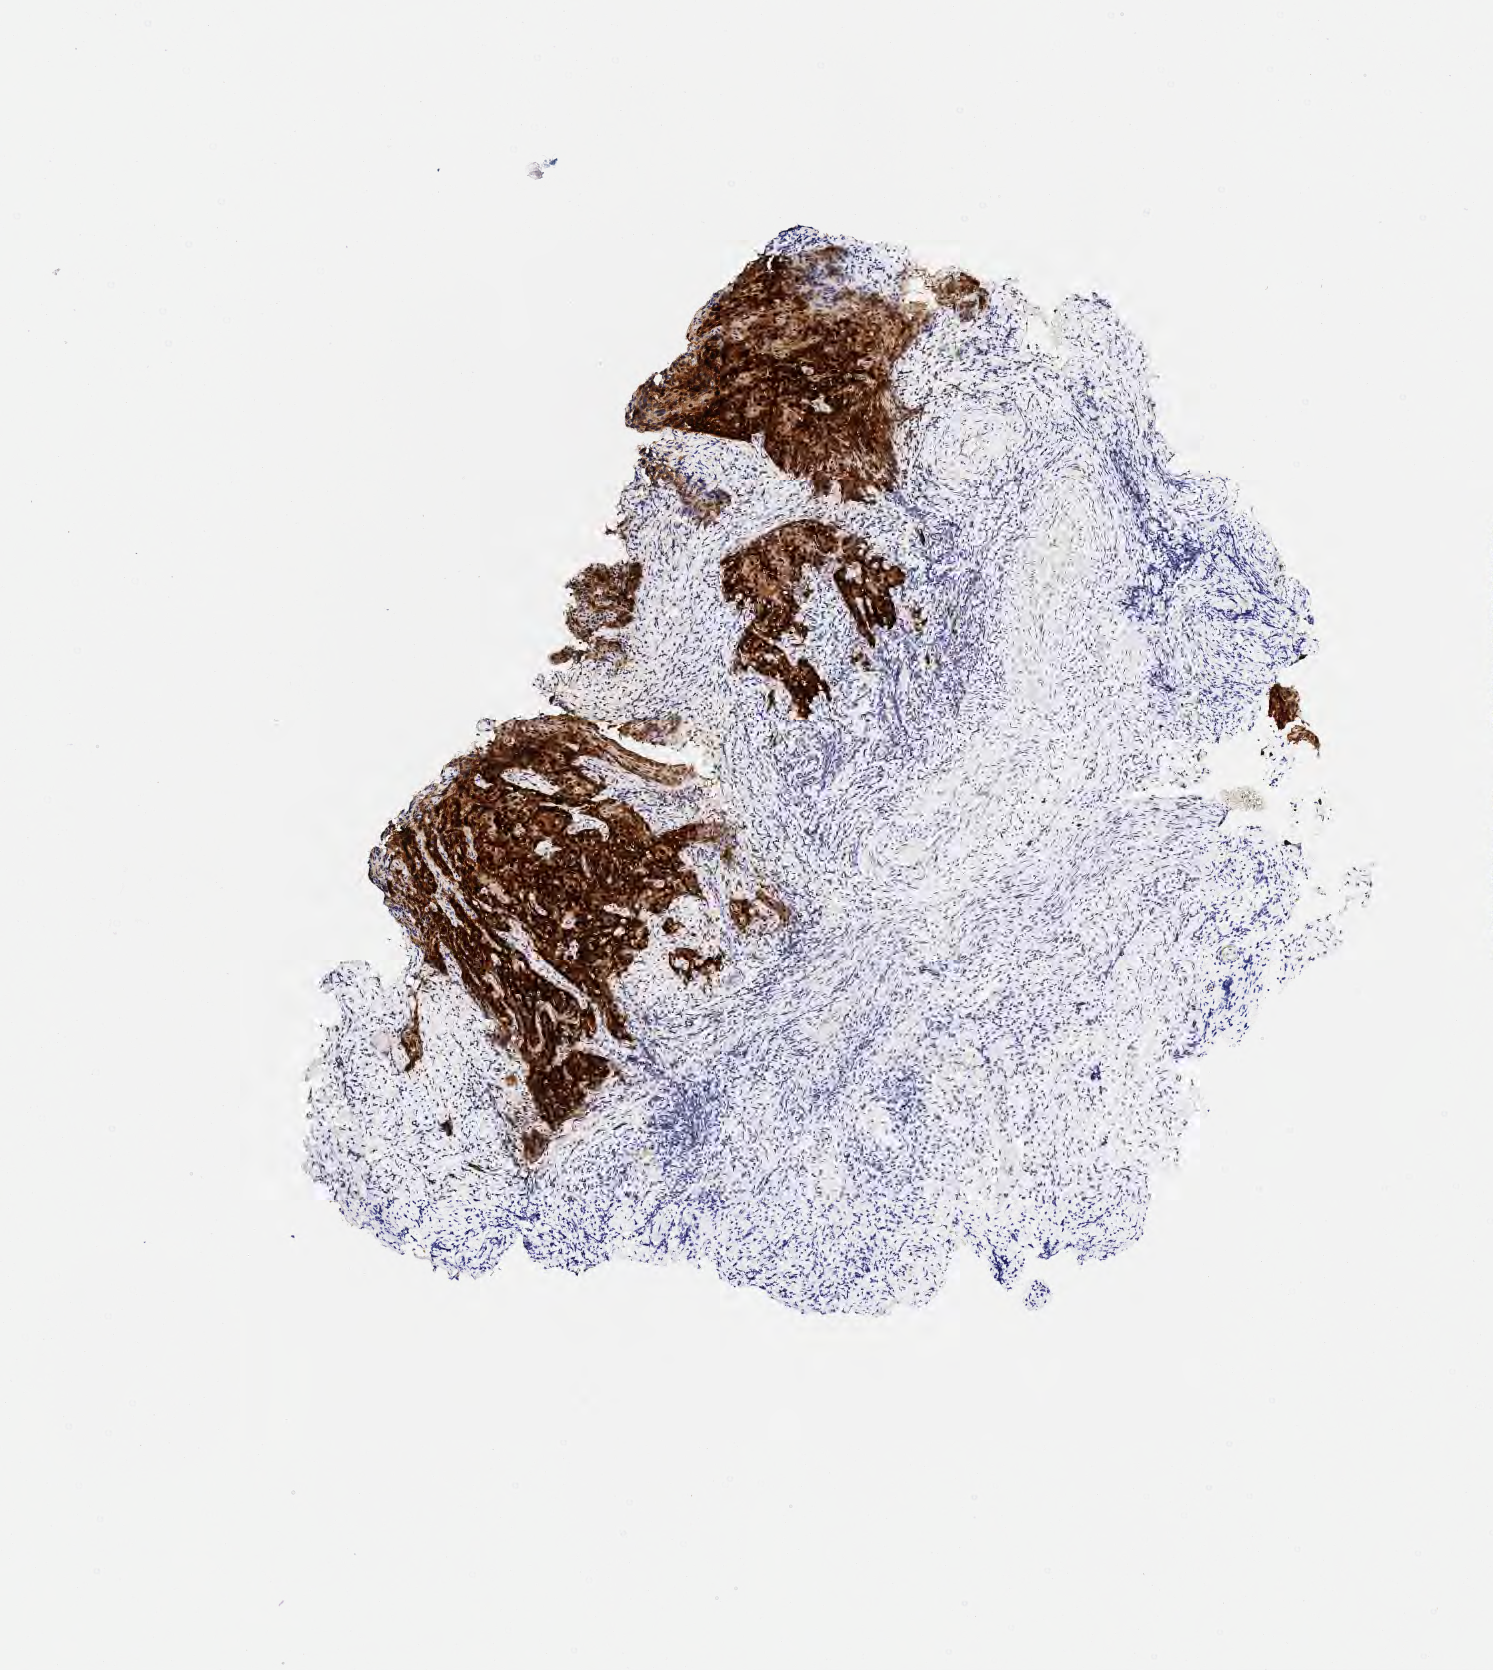
Immunohistochemistry (IHC) whole-slide image stained for p16 (p16INK4a), low-resolution overview of the scanned area, about 3.0 x 3.4 mm. Tumor tissue. Site: cervix. Patient: female, aged 58.
Histologic diagnosis: Squamous cell carcinoma, large cell, nonkeratinizing, NOS.